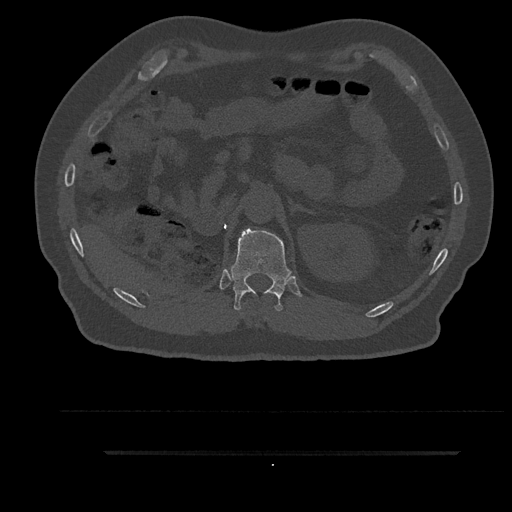
CT including the spine, one axial slice. Slice 250 of 797 in the series (ordered by position). Bone window (W 1800 / L 400 HU). 0.5 mm slice thickness. 512 × 512 image matrix, field of view 432 × 432 mm. Patient: male, 63 years. Case-level facts recorded for this patient, not image findings: primary cancer: renal; vertebrae with lytic lesions (as recorded): T8.
Outlined on this slice (semi-automatic segmentation, software-assisted and operator-edited):
- T12 vertebra: bounding box <228,228,292,311> (left, top, right, bottom; pixels)